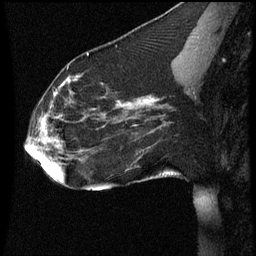
Breast MRI (dynamic contrast-enhanced), one sagittal slice; slice 25 of 60 in the series (ordered by position); dynamic contrast-enhanced series, image 2 of 3 at this slice position (ordered by acquisition); 1.5 T; TE 4.2 ms, TR 8.9 ms; 2 mm slice thickness; 256 × 256 image matrix. Female patient, age 35 years. From the clinical record (not read from this slice): setting: breast cancer imaged before/during neoadjuvant chemotherapy; receptor status: HER2-positive.
Annotated regions visible in this slice (semi-automatic segmentation, software-assisted and operator-edited):
- analysis volume of interest (the breast-tissue region the enhancement analysis was run in; not a lesion): bounding box [x1, y1, x2, y2] px = [23, 66, 177, 177]
- tumour enhancement mask (voxels above the 70 % enhancement threshold inside the analysis volume of interest): [36, 76, 156, 157]